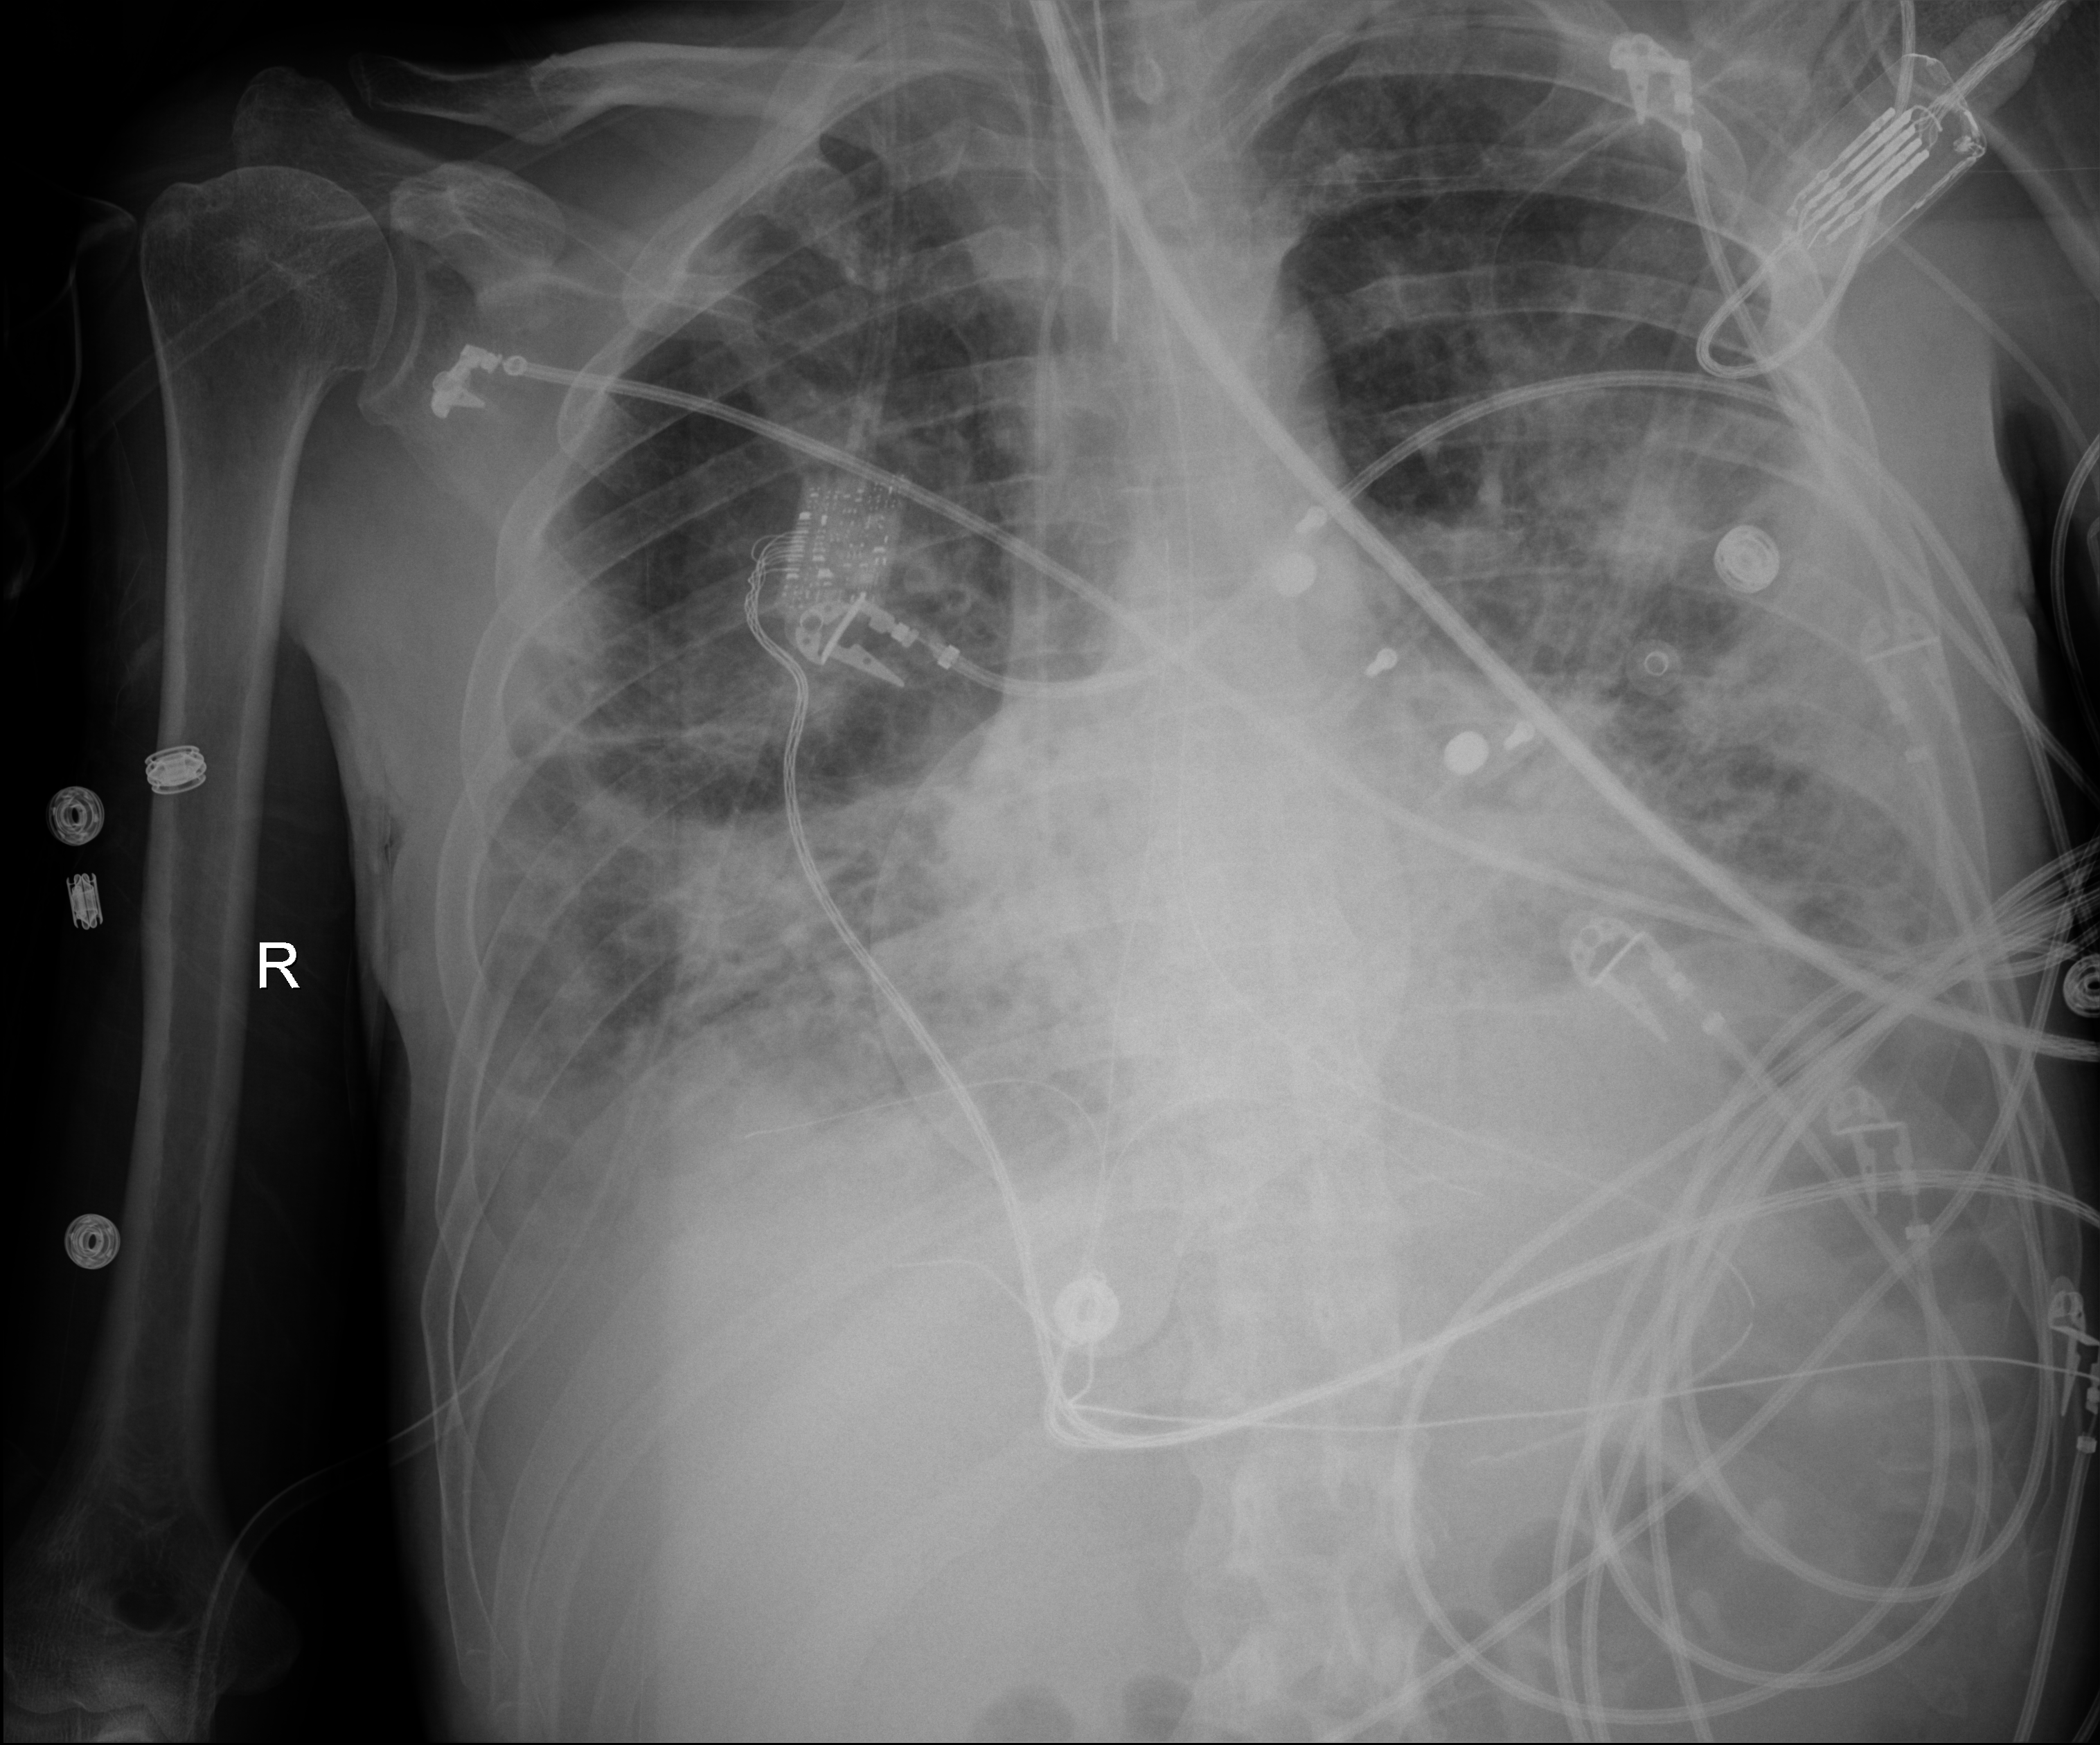
Chest X-ray (portable); anteroposterior (AP) projection. Patient hospitalised with COVID-19; male, aged 18–59 years.
Admission-level facts for this patient (not findings on this image; timing relative to this image not recorded):
- admitted to intensive care during this hospital stay: yes
- other chronic lung disease (admission record): no